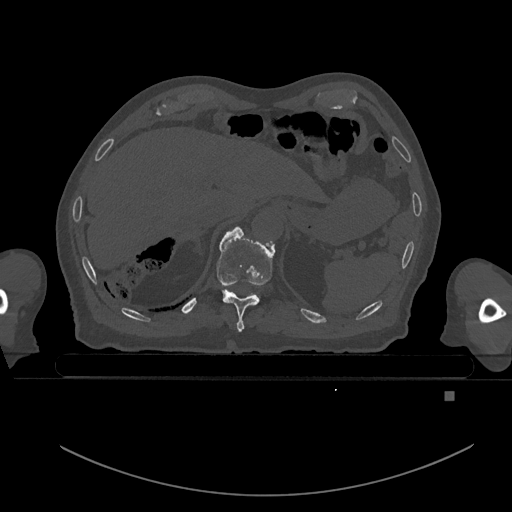
CT including the spine, one axial slice. Slice 80 of 969 in the series (ordered by position). Bone window (W 1800 / L 400 HU). 0.5 mm slice thickness. 512 × 512 image matrix. Patient: male, 82 years. Case-level facts recorded for this patient, not image findings: primary cancer: prostate; vertebrae with lytic lesions (as recorded): T11, T9, T8, T2.
Structures marked on this image (semi-automatic segmentation, software-assisted and operator-edited):
- T10 vertebra: box from (x=217, y=227) to (x=275, y=331) px